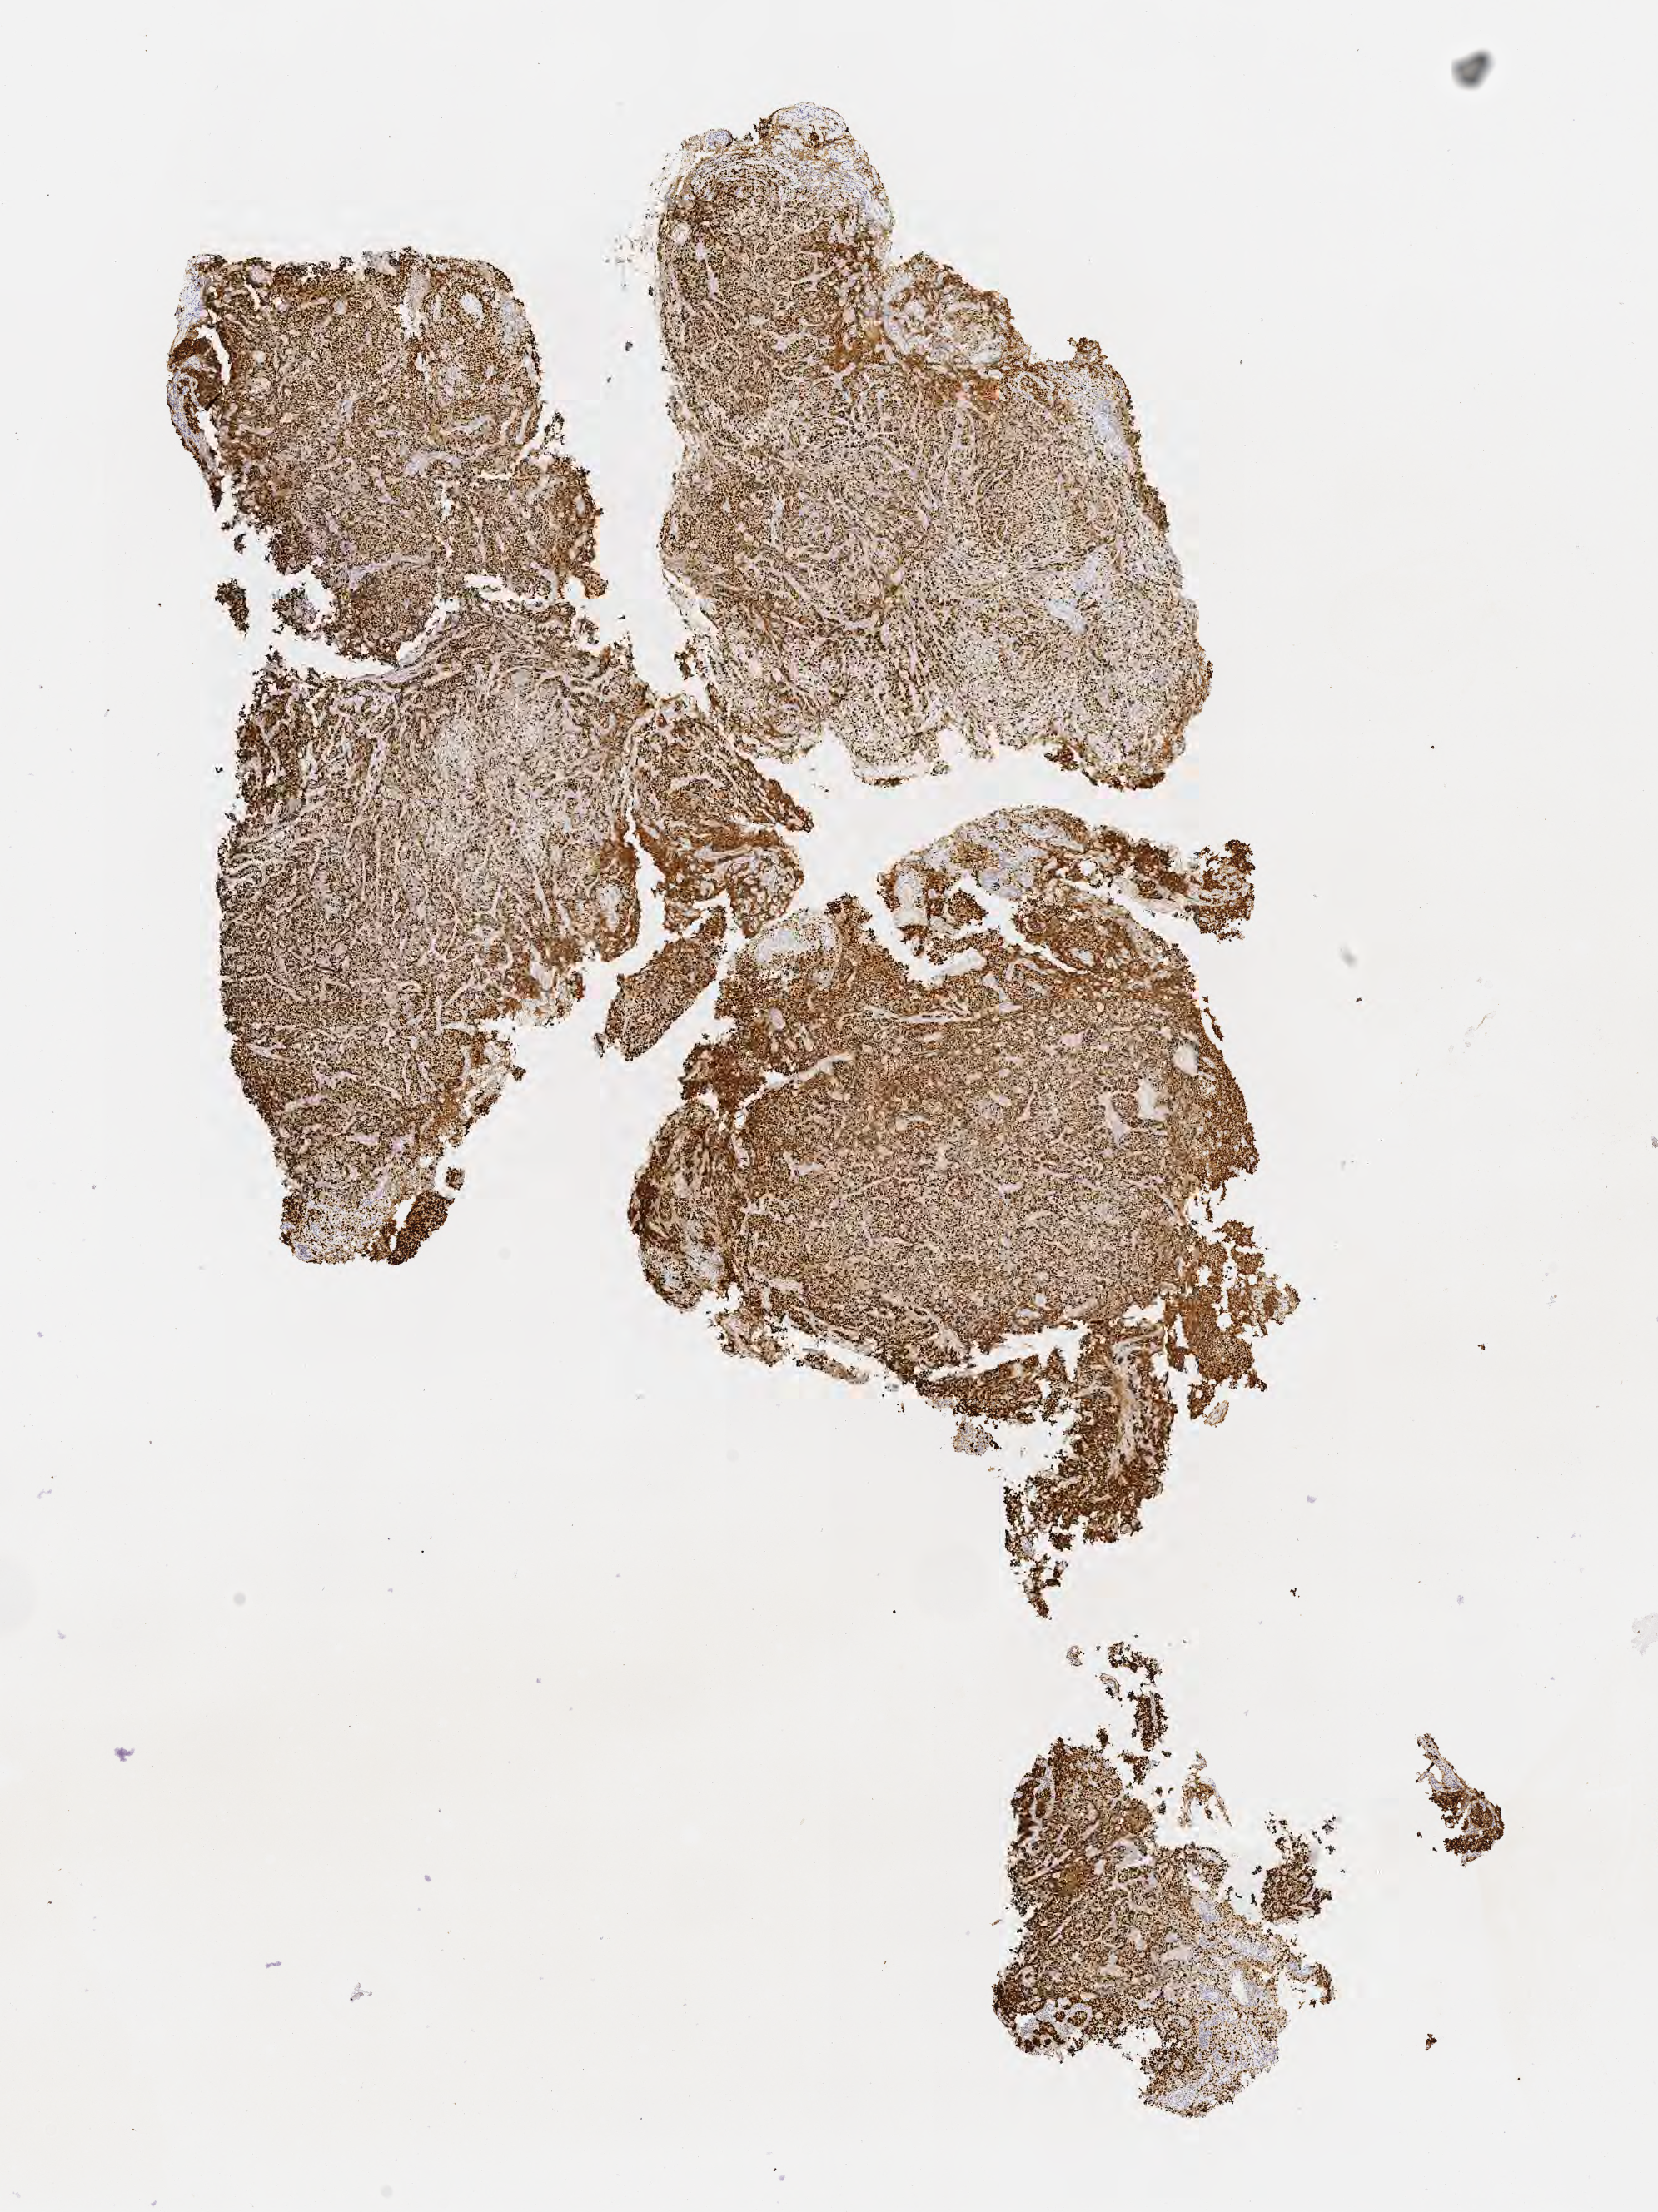
Immunohistochemistry (IHC) whole-slide image stained for p53, a low-resolution overview of the entire scanned area, about 8.1 x 10.7 mm. Specimen: tumor tissue. Anatomic site: cervix. Patient: female, aged 75.
Diagnosis: Adenocarcinoma, NOS.